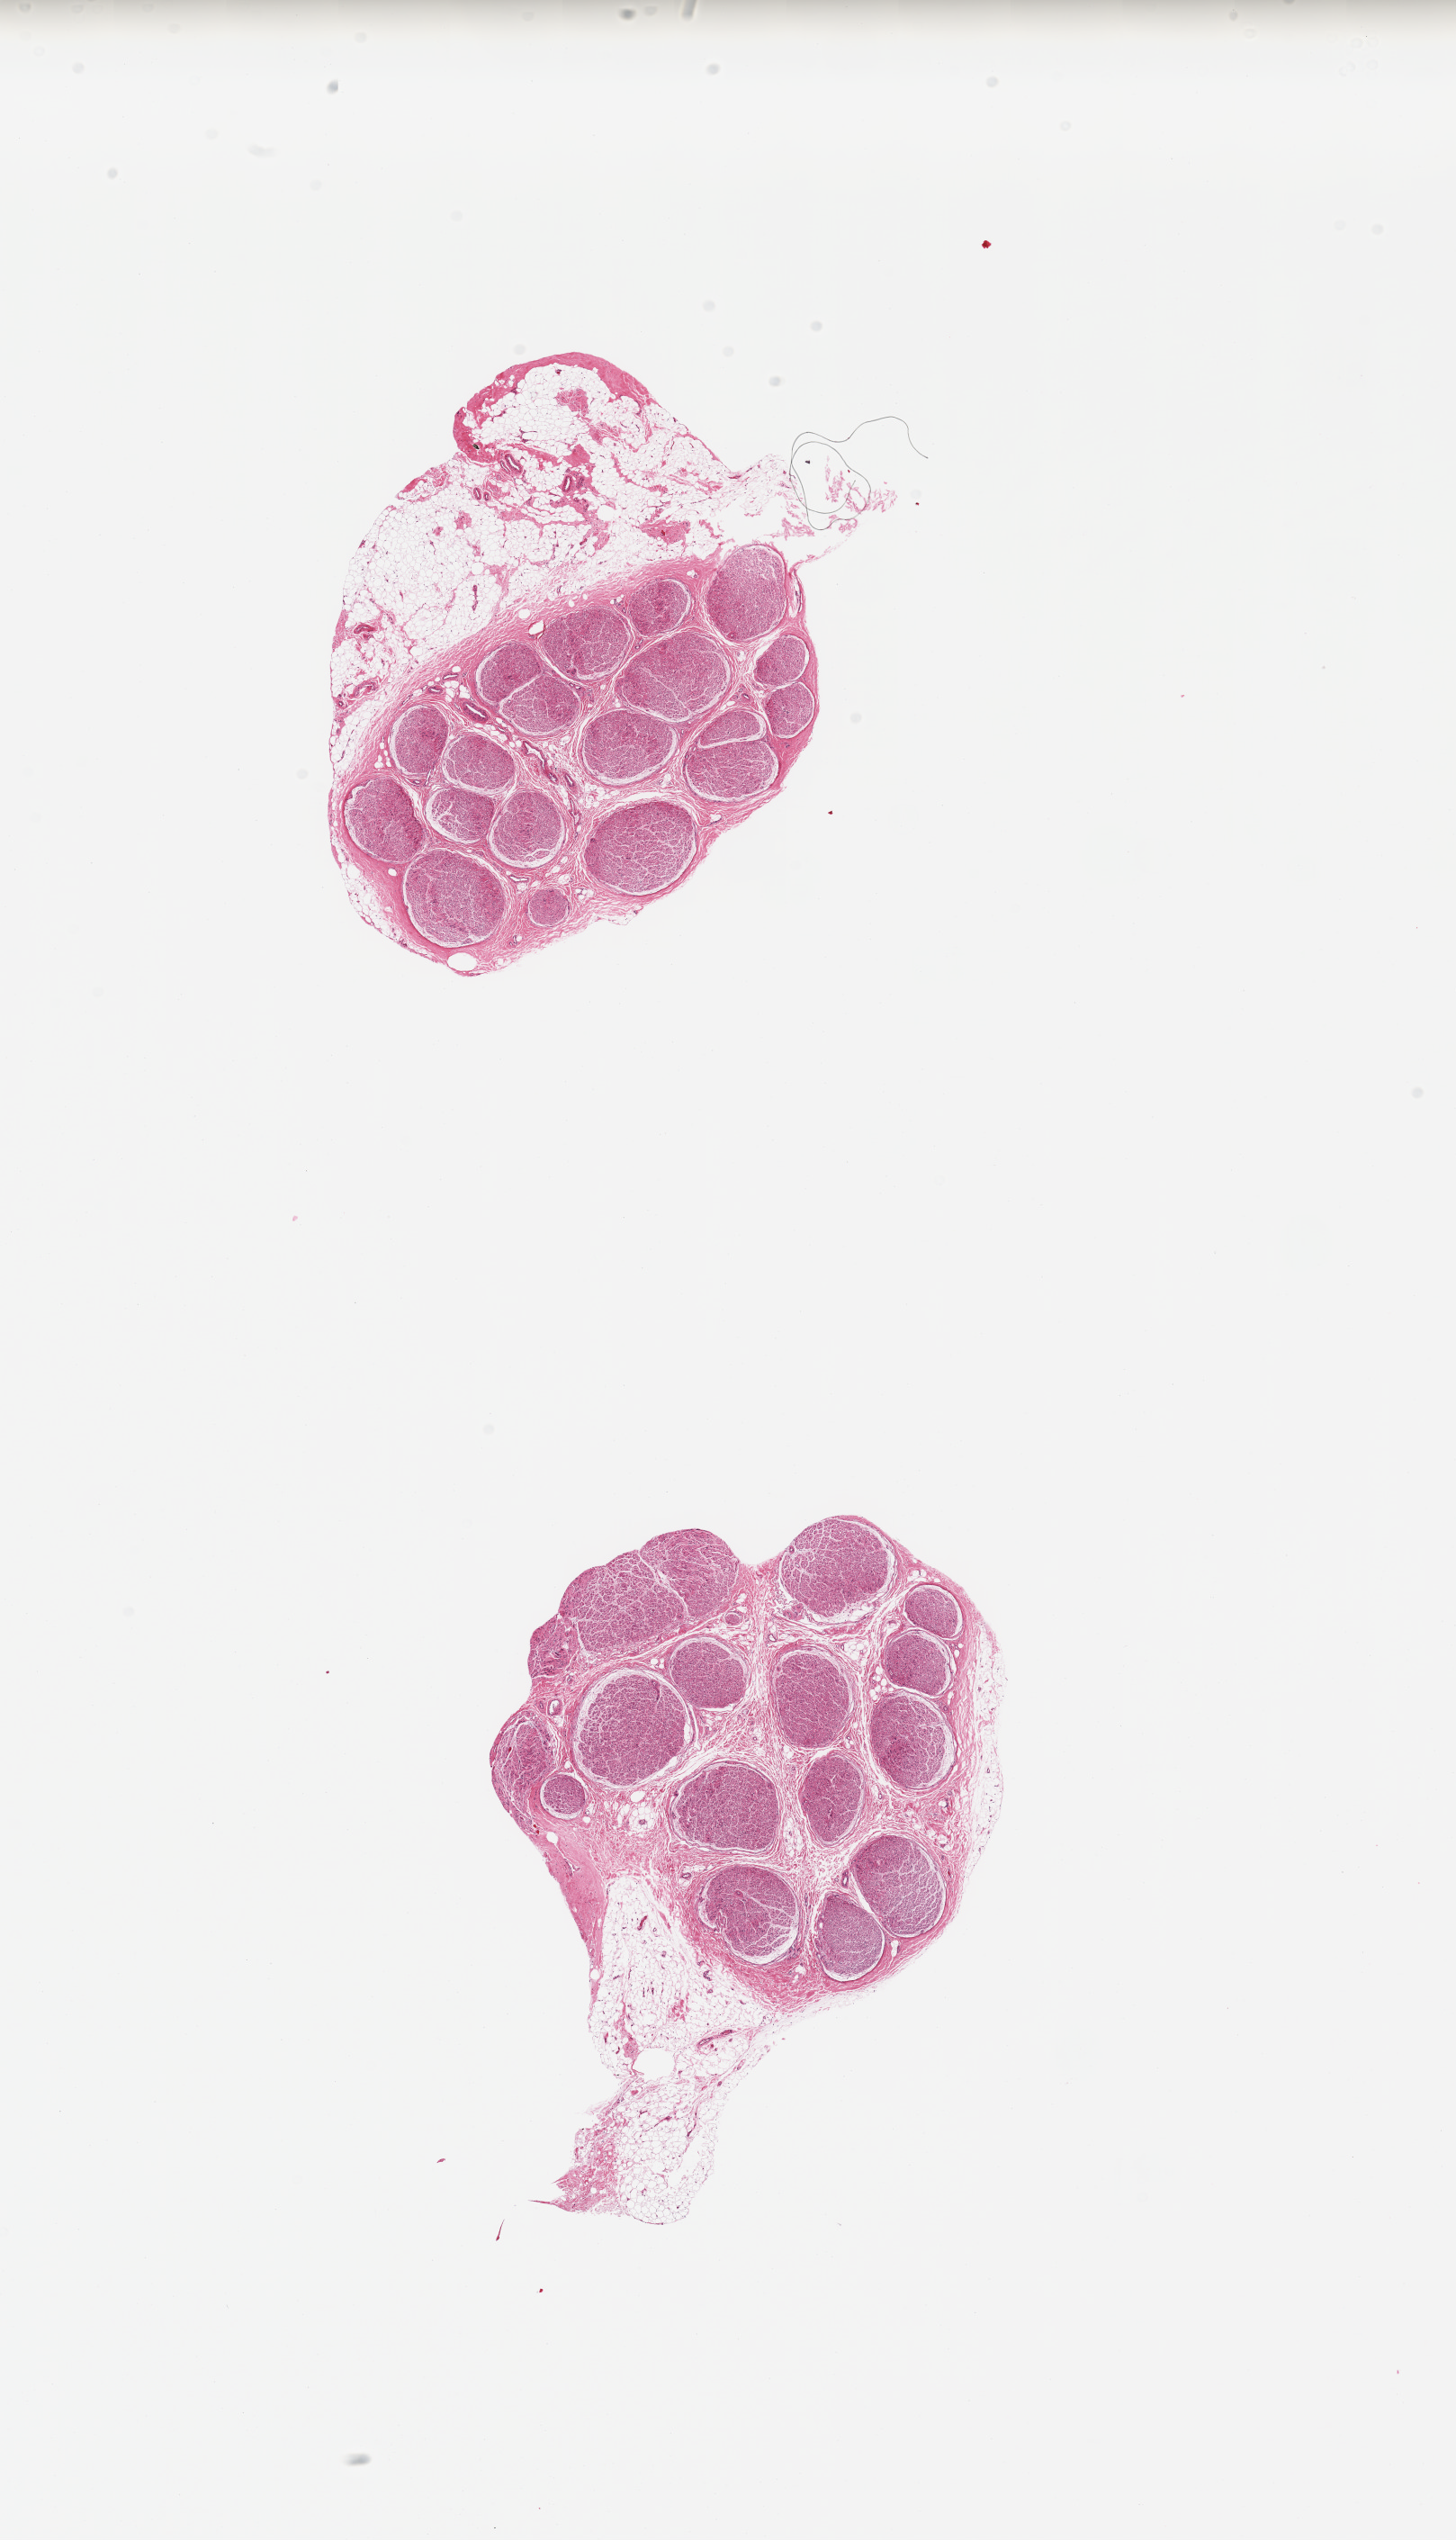
Whole-slide image, hematoxylin and eosin (H&E) stain — a low-resolution overview of the entire scanned area, about 12.8 x 22.3 mm. PAXgene-fixed paraffin-embedded (PFPE) section. Sampled site (target tissue): tibial nerve. Donor tissue sample. Donor sex: female.
• reviewer comment on this tissue sample: 2 pieces, adherent fatty nubbins up to ~2.5mm, ~30-35% of total tissue. Sample with care